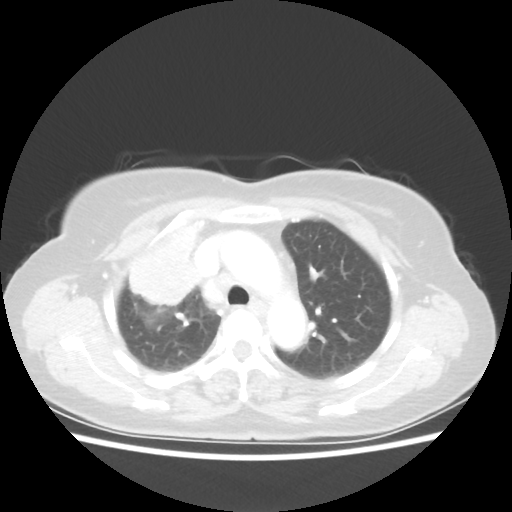
Chest CT, one axial slice. Position 39 of 55 along the scan axis. Lung window (W 1500 / L -600 HU). 512 × 512 image matrix, field of view 337 × 337 mm. Patient: female, 62 years. Case-level facts recorded for this patient, not image findings: clinical TNM (as recorded): T4 N3 M0.
Outlined on this slice (bounding box drawn by a radiologist):
- lung tumour (recorded histology: squamous cell carcinoma): bounding box <116,233,208,308> (left, top, right, bottom; pixels)